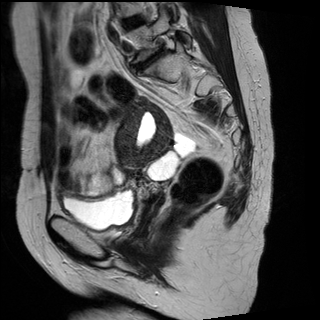
Pelvic MRI for cervical cancer, one sagittal slice; slice 12 of 29 in the series (ordered by position); T2-weighted; 1.5 T; TE 89 ms, TR 2930 ms; 4 mm slice thickness; 320 × 320 image matrix. Patient: female, 45 years.
Annotated regions visible in this slice (outlined manually by an expert reader):
- uterus and cervix: bounding box <115,97,174,180> (left, top, right, bottom; pixels)